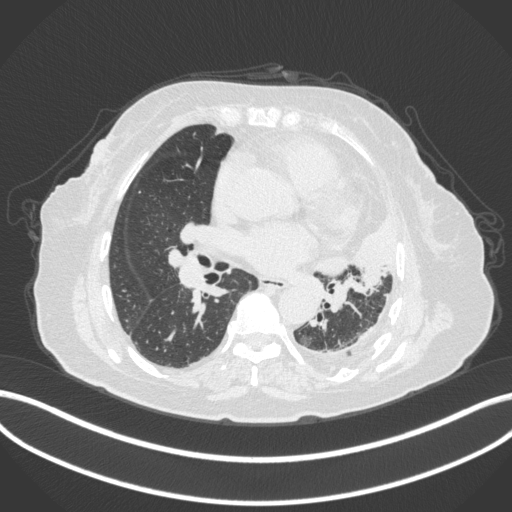
Chest CT, one axial slice; slice 182 of 399 in the series (ordered by position); 120 kVp; lung window (W 1500 / L -600 HU); 1 mm slice thickness; 512 × 512 image matrix, field of view 400 × 400 mm. Patient: female, 75 years. Case-level facts recorded for this patient, not image findings: clinical TNM (as recorded): T3 N3 M1.
Annotated regions visible in this slice (bounding box drawn by a radiologist):
- lung tumour (recorded histology: adenocarcinoma): bounding box (x1, y1, x2, y2) in pixels: (317, 215, 401, 283)